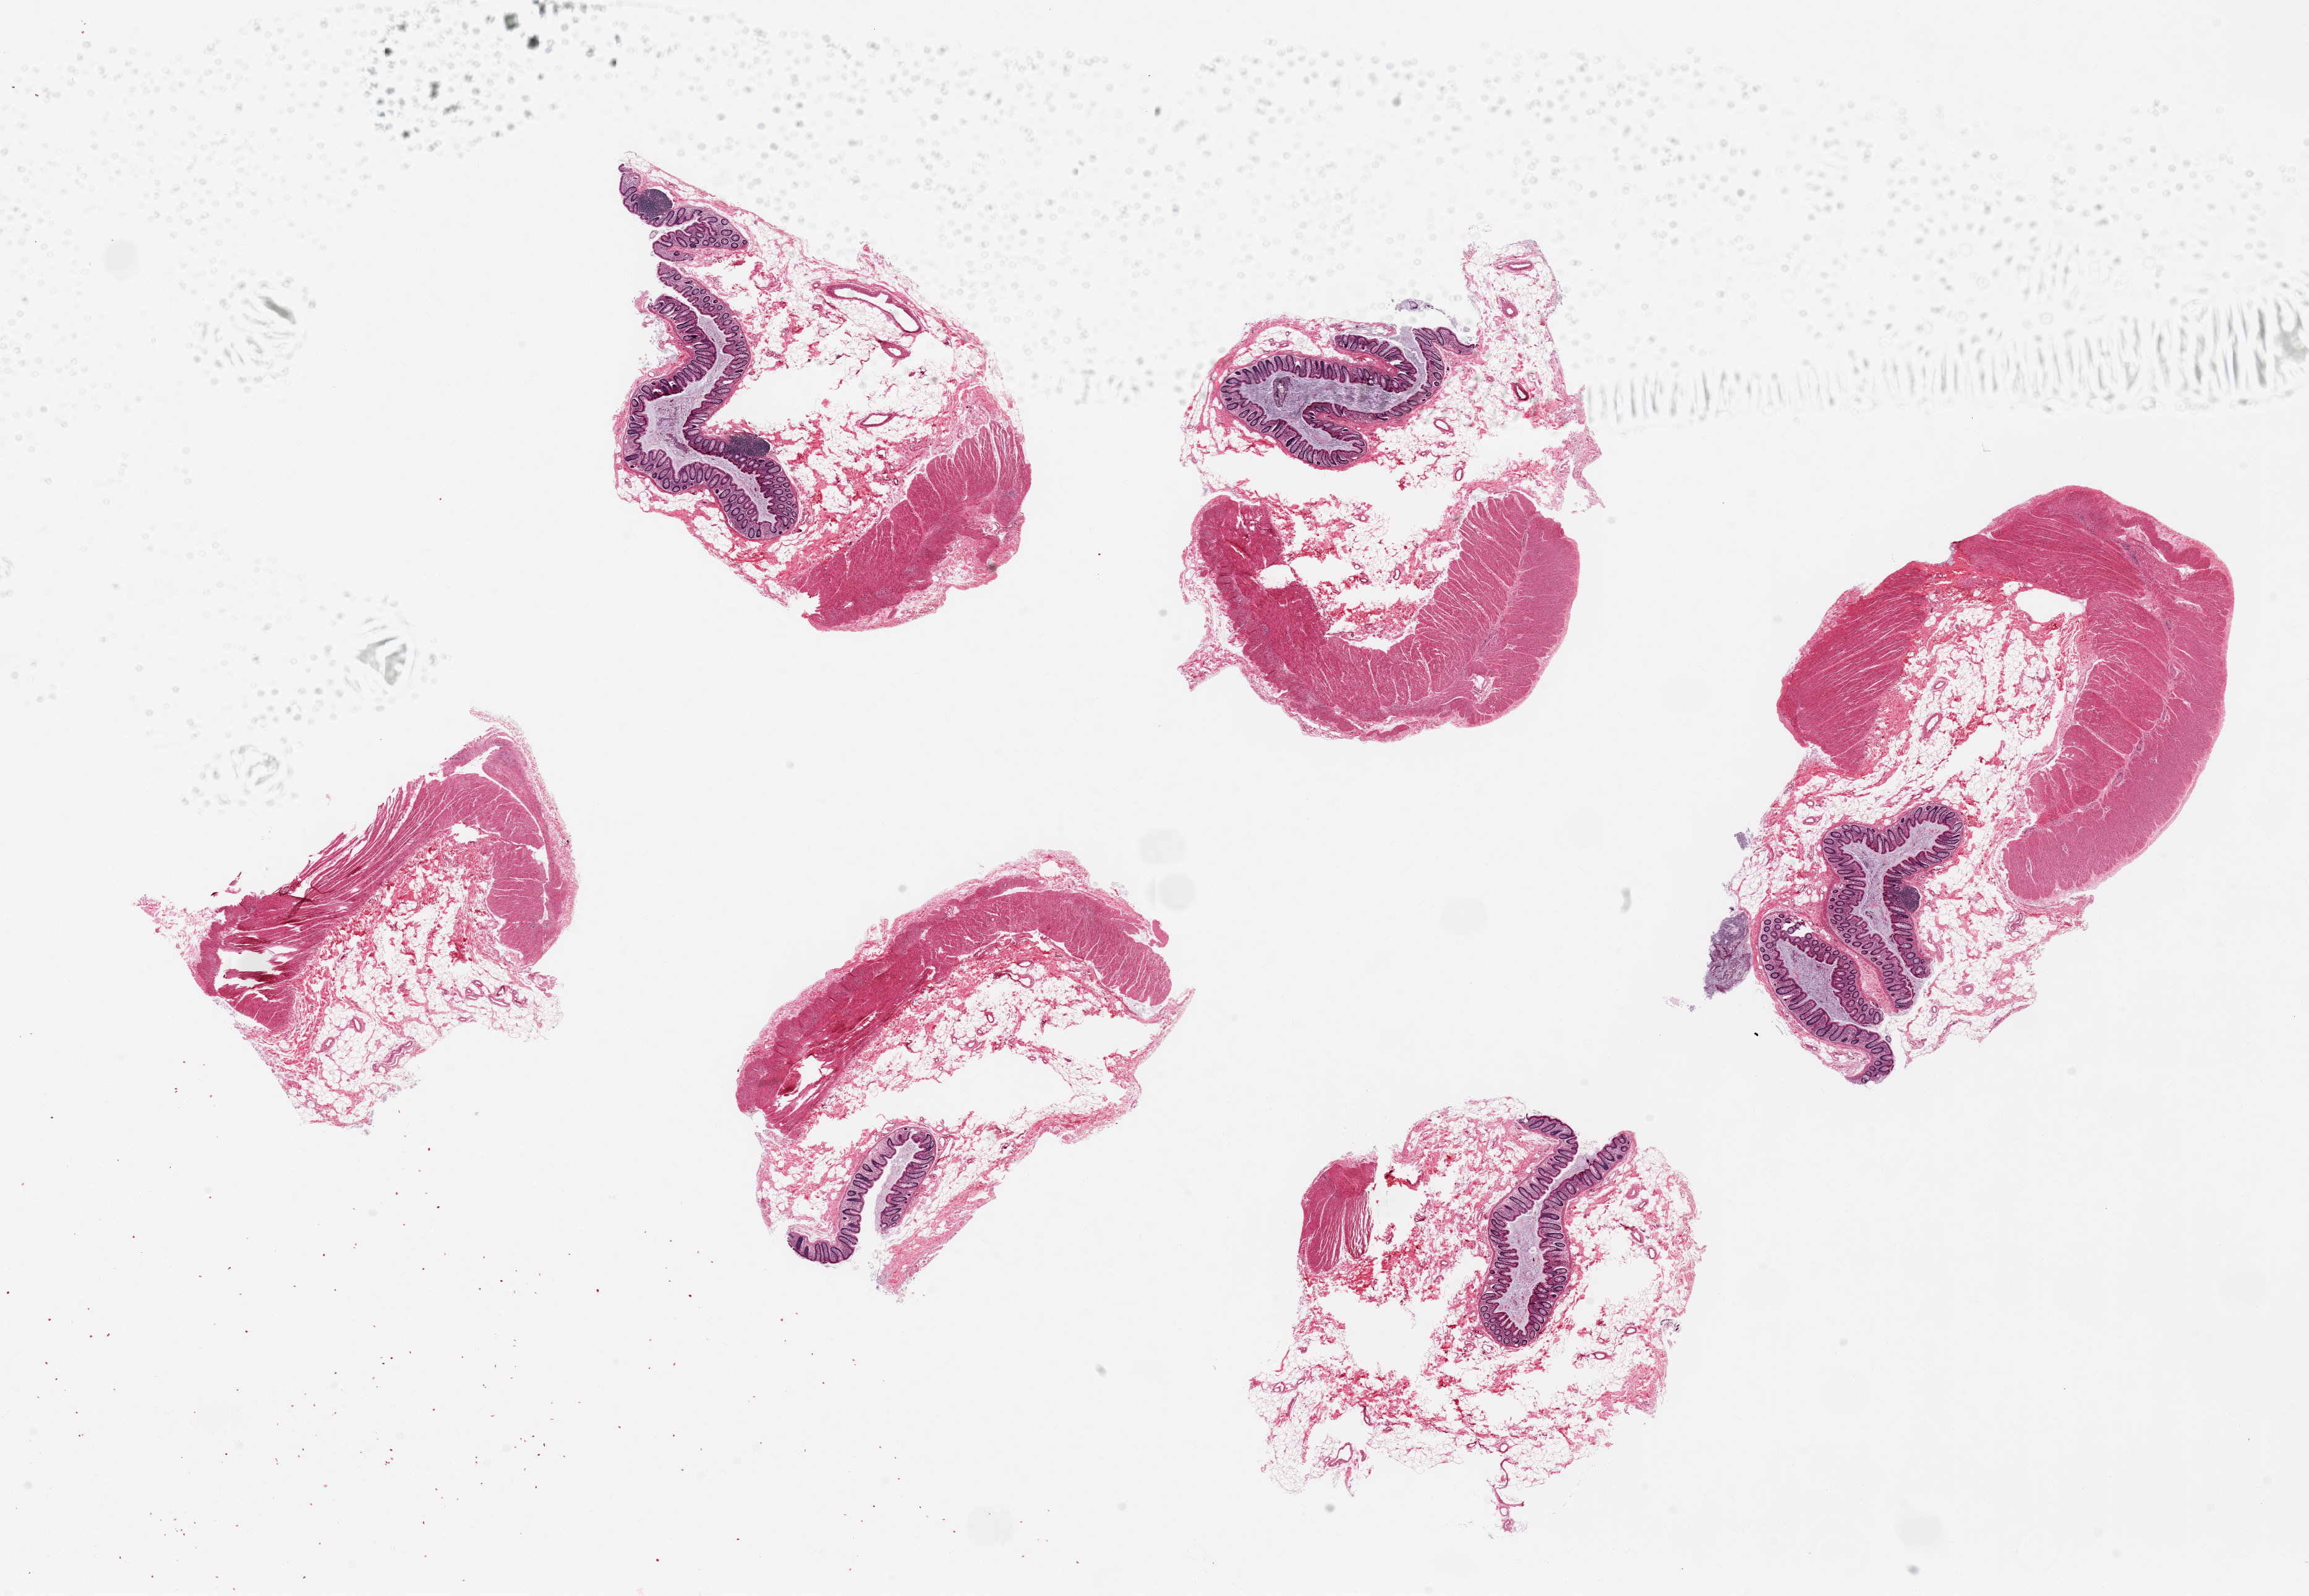
H&E whole-slide image, shown as a low-resolution overview of the whole scanned area (about 29.5 x 20.4 mm, acquisition: 20x scan), PAXgene-fixed, paraffin-embedded tissue, sampled site (target tissue): transverse colon, tissue donor sample. Donor sex: male.
• reviewer comment on this tissue sample: 6 pieces up to 8x5 mm; 5 of 6 have mucosa